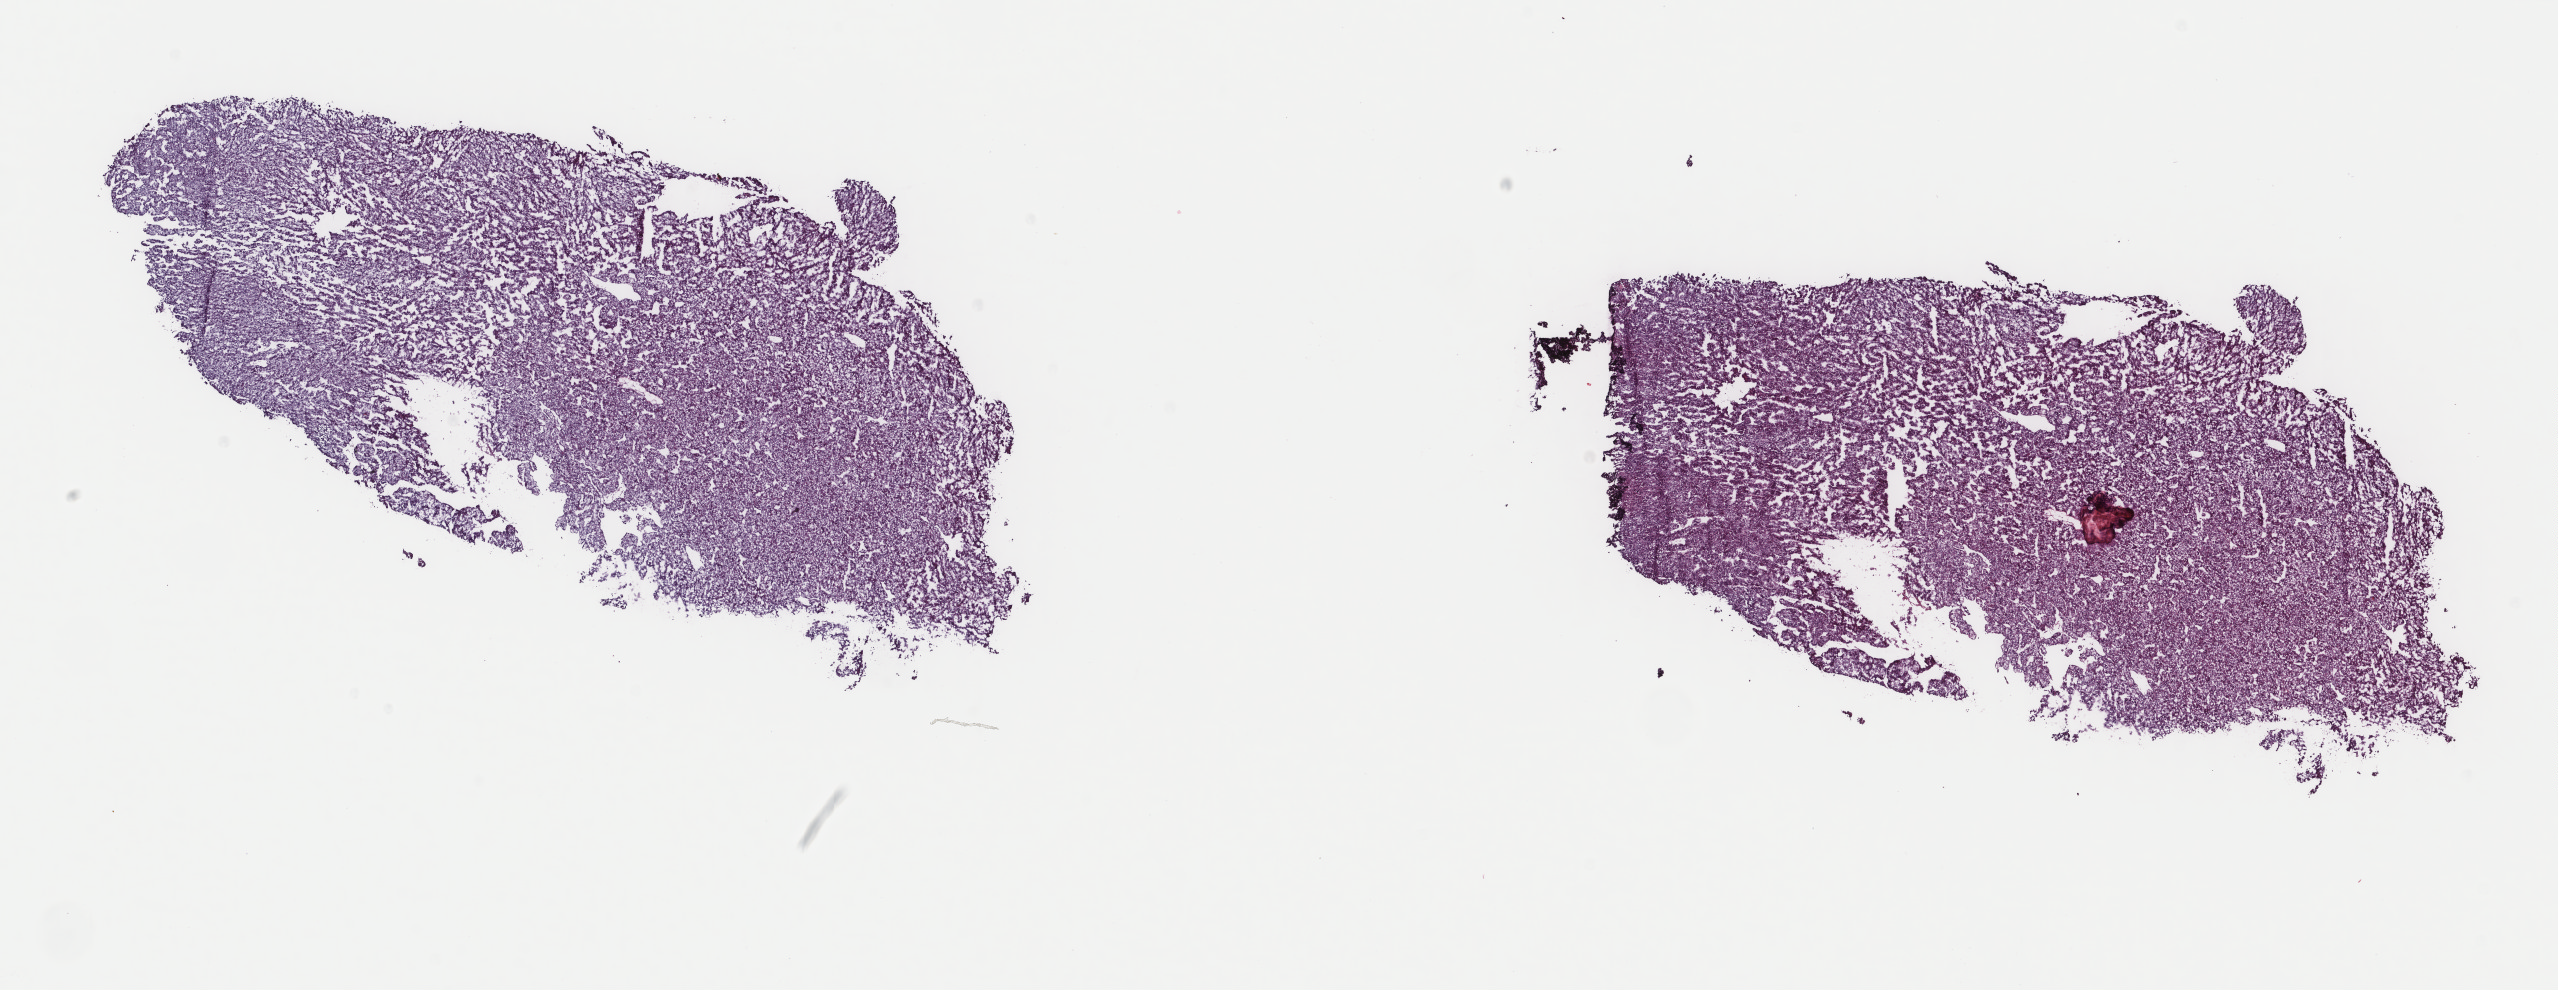
Whole-slide histology image, Hematoxylin and eosin (H&E) stained, whole scanned area (about 20.3 x 7.9 mm) shown as a low-resolution overview; frozen section from the top of the tissue portion; primary tumour sample from the liver. Female, age 79 years at initial diagnosis. Histologic grade: G2 (moderately differentiated). Slide review estimates, as recorded: tumour cells 92%, tumour nuclei 92%, normal cells 0%, stromal cells 5%, necrosis 3%. Inflammatory infiltration, as recorded: lymphocyte infiltration 3%, monocyte infiltration 1%, neutrophil infiltration 0%.
• histologic diagnosis: Hepatocellular carcinoma, NOS
• AJCC pathologic stage: II (7th edition)